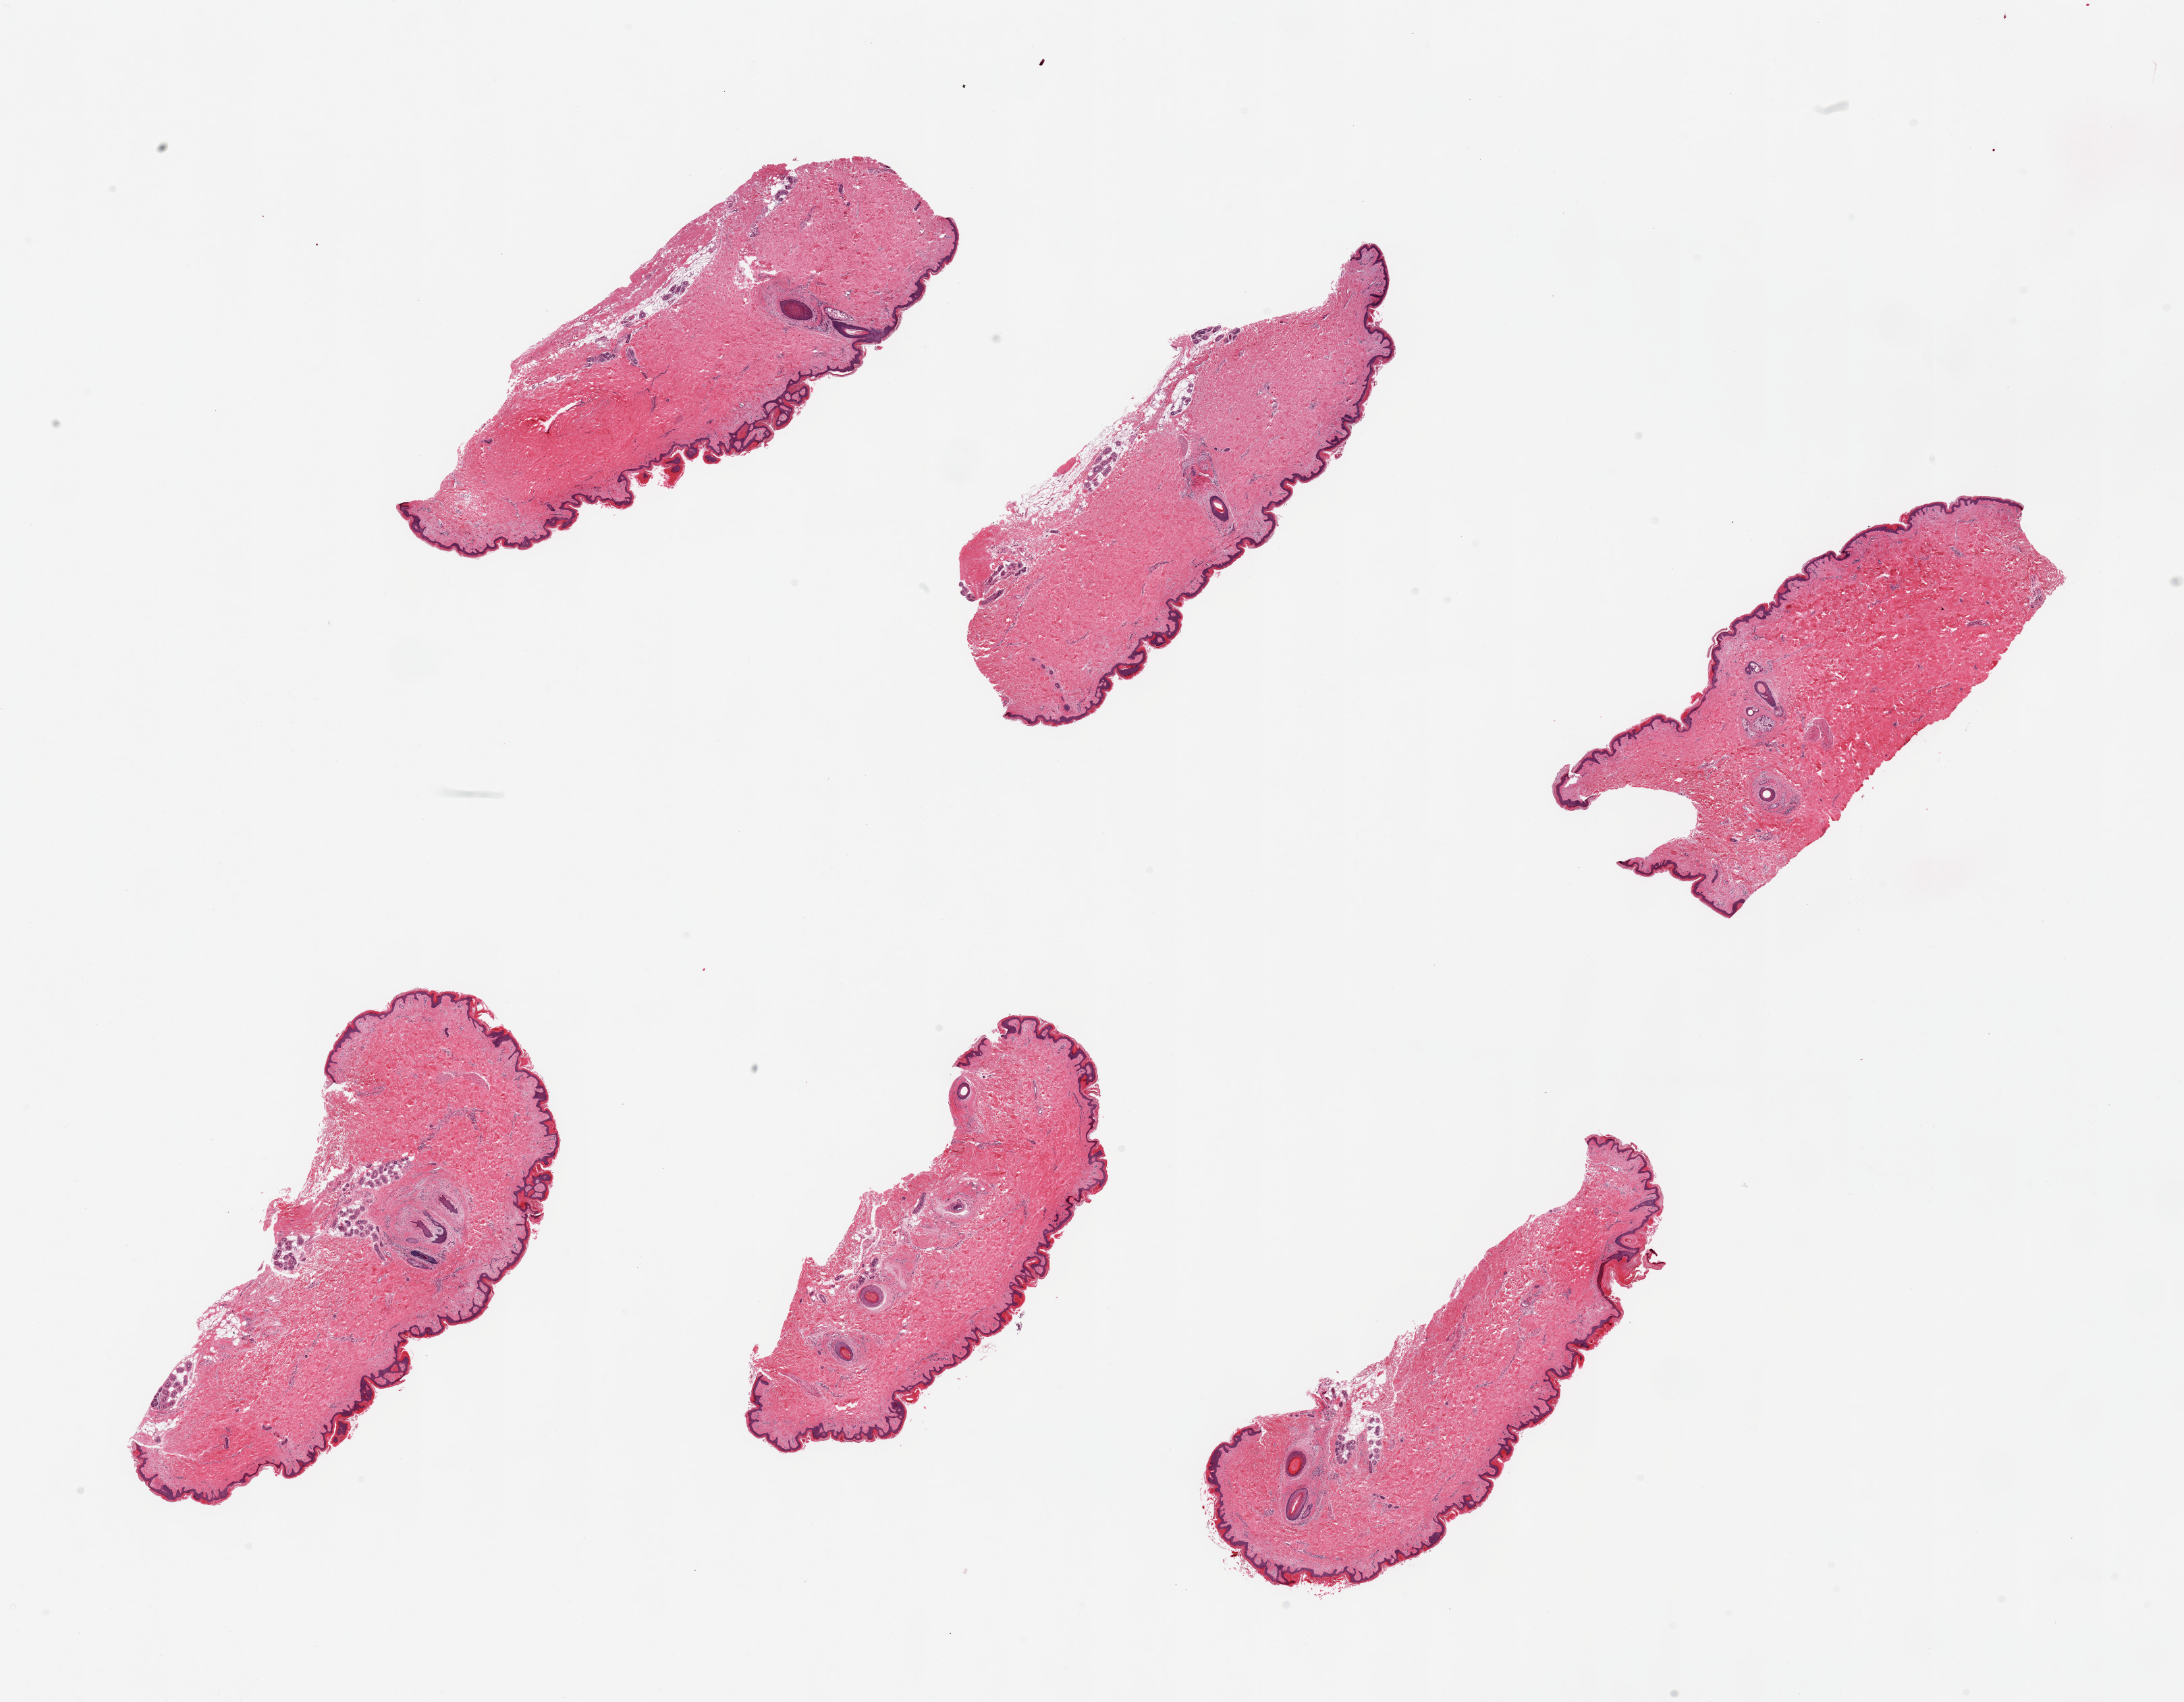
Digitized hematoxylin and eosin (H&E)-stained section — shown as a low-resolution overview of the whole scanned area (about 25.6 x 19.9 mm, slide scanned at 20x). PAXgene-fixed paraffin-embedded (PFPE) section. Section of skin of suprapubic region (target tissue). Tissue donor sample. Donor sex: female.
Pathologist's review note for this sample: 6 pieces, minimal dermal fat, squamous epithelium is ~30 microns.